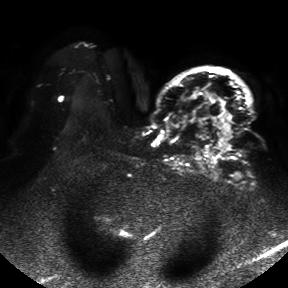
Breast MRI, one axial slice; position 33 of 50 along the scan axis; diffusion-weighted series; image 2 of 4 stored at this slice position (different b-values; order by instance number); 1.5 T; 288 × 288 image matrix. Female patient.
Annotated regions visible in this slice (expert manual segmentation):
- tumour on diffusion-weighted imaging: bounding box (x1, y1, x2, y2) in pixels: (190, 91, 233, 151)